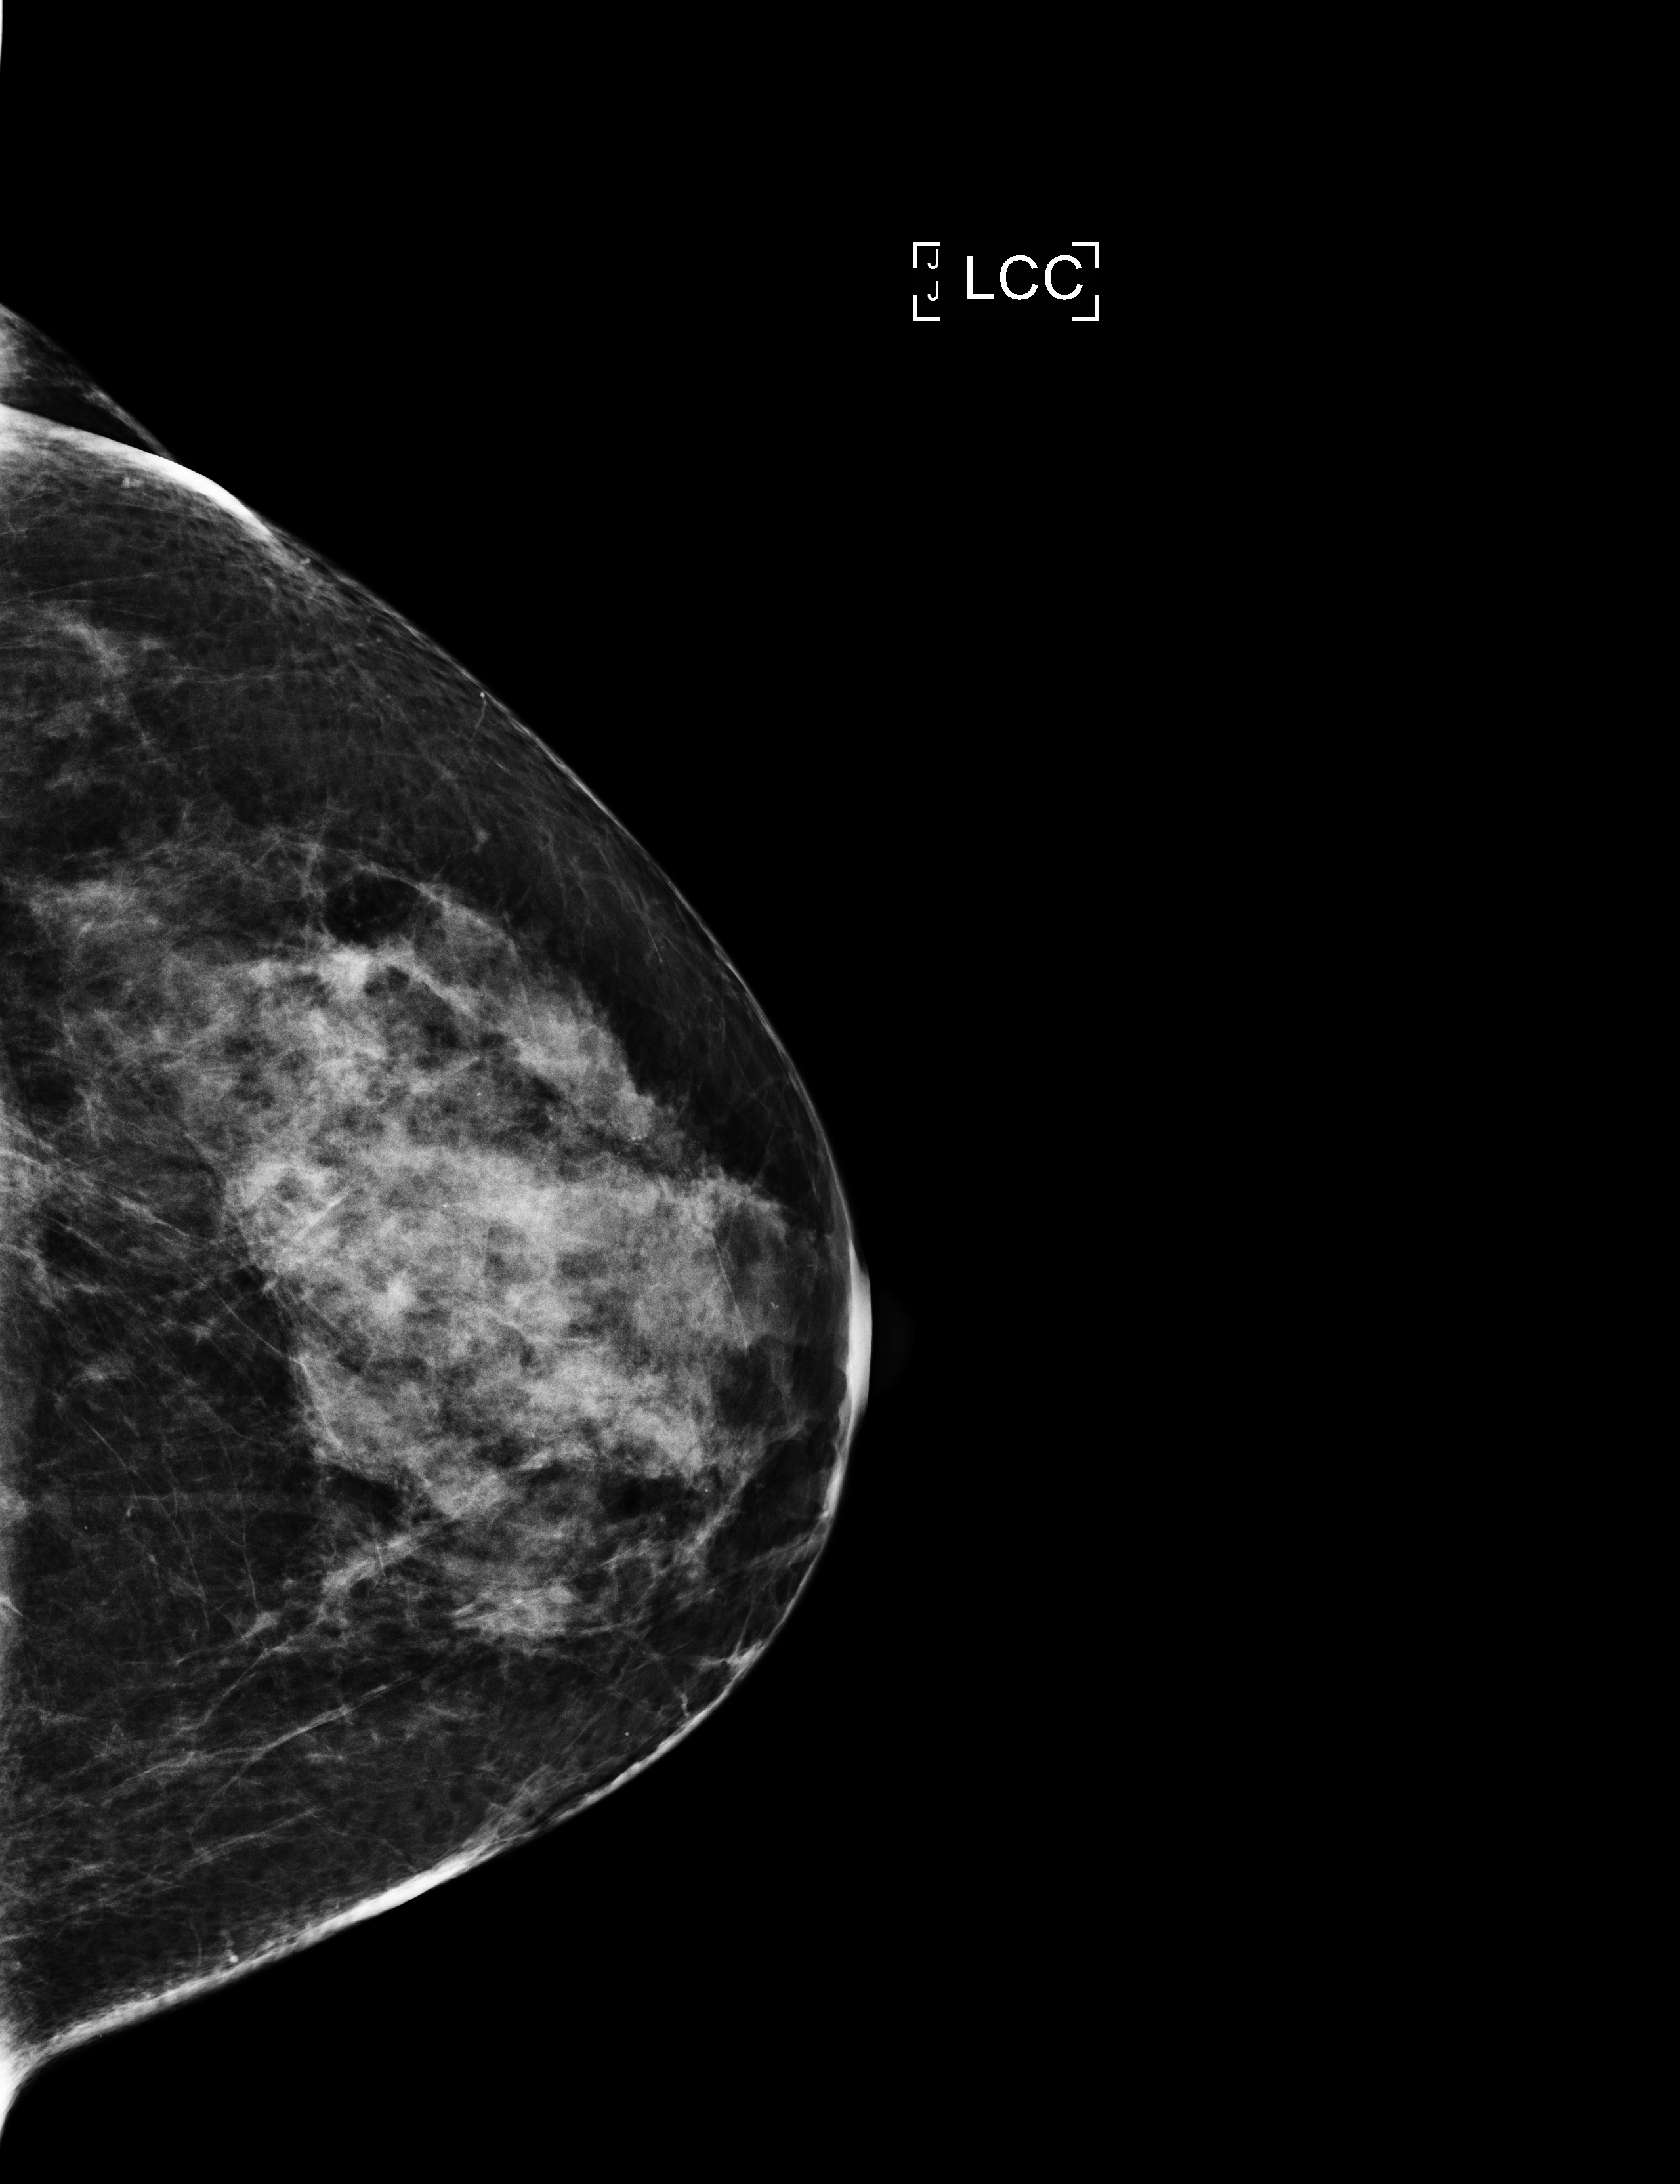
Digital mammogram (FFDM), left breast, cranio-caudal projection, annual screening mammography examination, compressed breast thickness 67 mm. Patient aged 55 years (female).
Breast density at the screening exam (both breasts): heterogeneously dense (BI-RADS density category c).